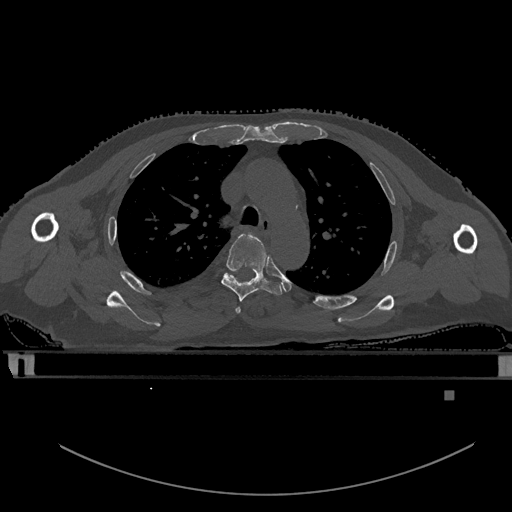
CT including the spine, one axial slice; slice 406 of 969 in the series (ordered by position); bone window (W 1800 / L 400 HU); 0.5 mm slice thickness; 512 × 512 image matrix. Patient: male, 82 years. Case-level facts recorded for this patient, not image findings: primary cancer: prostate; vertebrae with lytic lesions (as recorded): T11, T9, T8, T2.
Annotated regions visible in this slice (semi-automatic segmentation, software-assisted and operator-edited):
- T3 vertebra: bounding box [x1, y1, x2, y2] px = [235, 307, 241, 314]
- T4 vertebra: [221, 233, 282, 302]
- T5 vertebra: [223, 273, 236, 281]